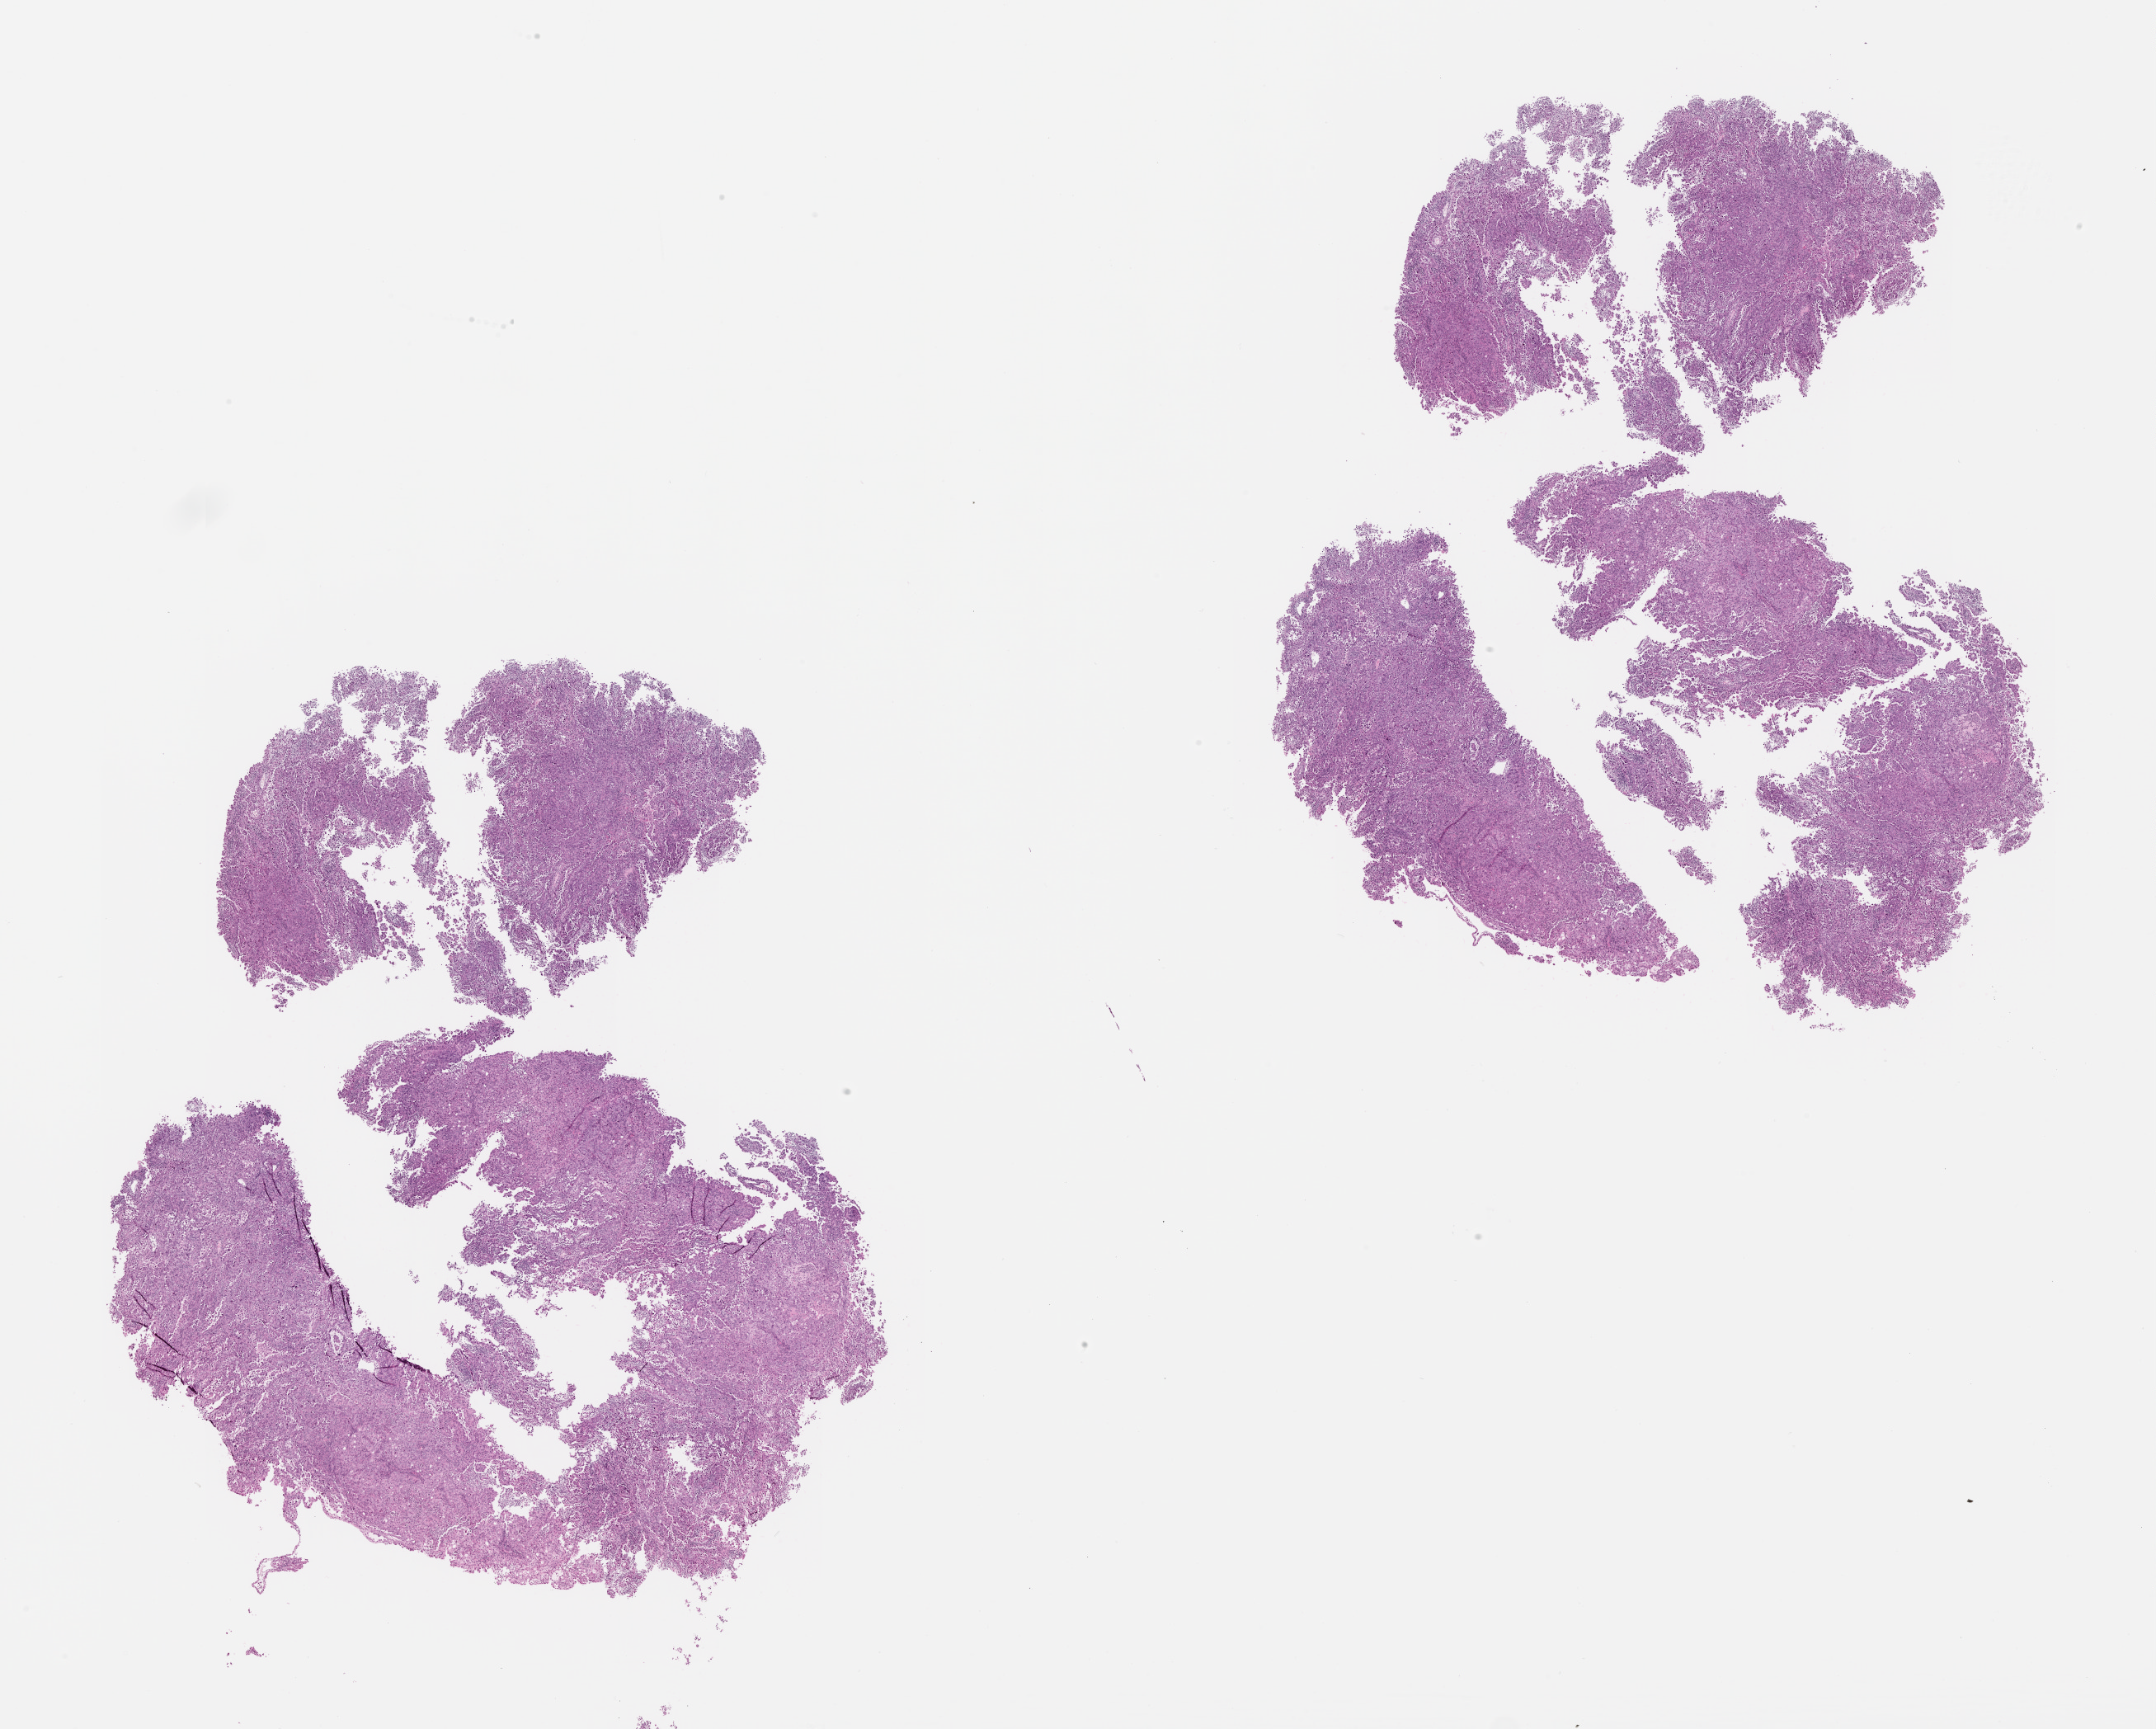
H&E whole-slide image — low-resolution overview of the scanned area, about 21.0 x 16.9 mm. Uterus, tissue type not recorded.
* patient diagnosis (cohort enrolment): corpus endometrial carcinoma (uterus)